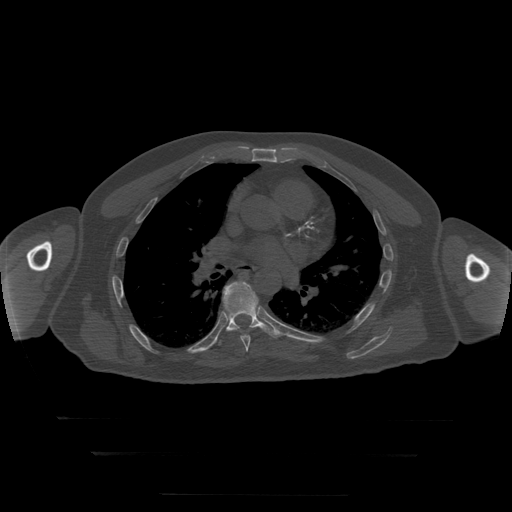
CT including the spine, one axial slice; slice 176 of 397 in the series (ordered by position); reconstruction kernel STANDARD; bone window (W 1800 / L 400 HU); 1.25 mm slice thickness; 512 × 512 image matrix. Patient age 73 years. Case-level facts recorded for this patient, not image findings: primary cancer: prostate.
Annotated regions visible in this slice (semi-automatic segmentation, software-assisted and operator-edited):
- T7 vertebra: bounding box <241,335,251,352> (left, top, right, bottom; pixels)
- T8 vertebra: <212,282,282,346>